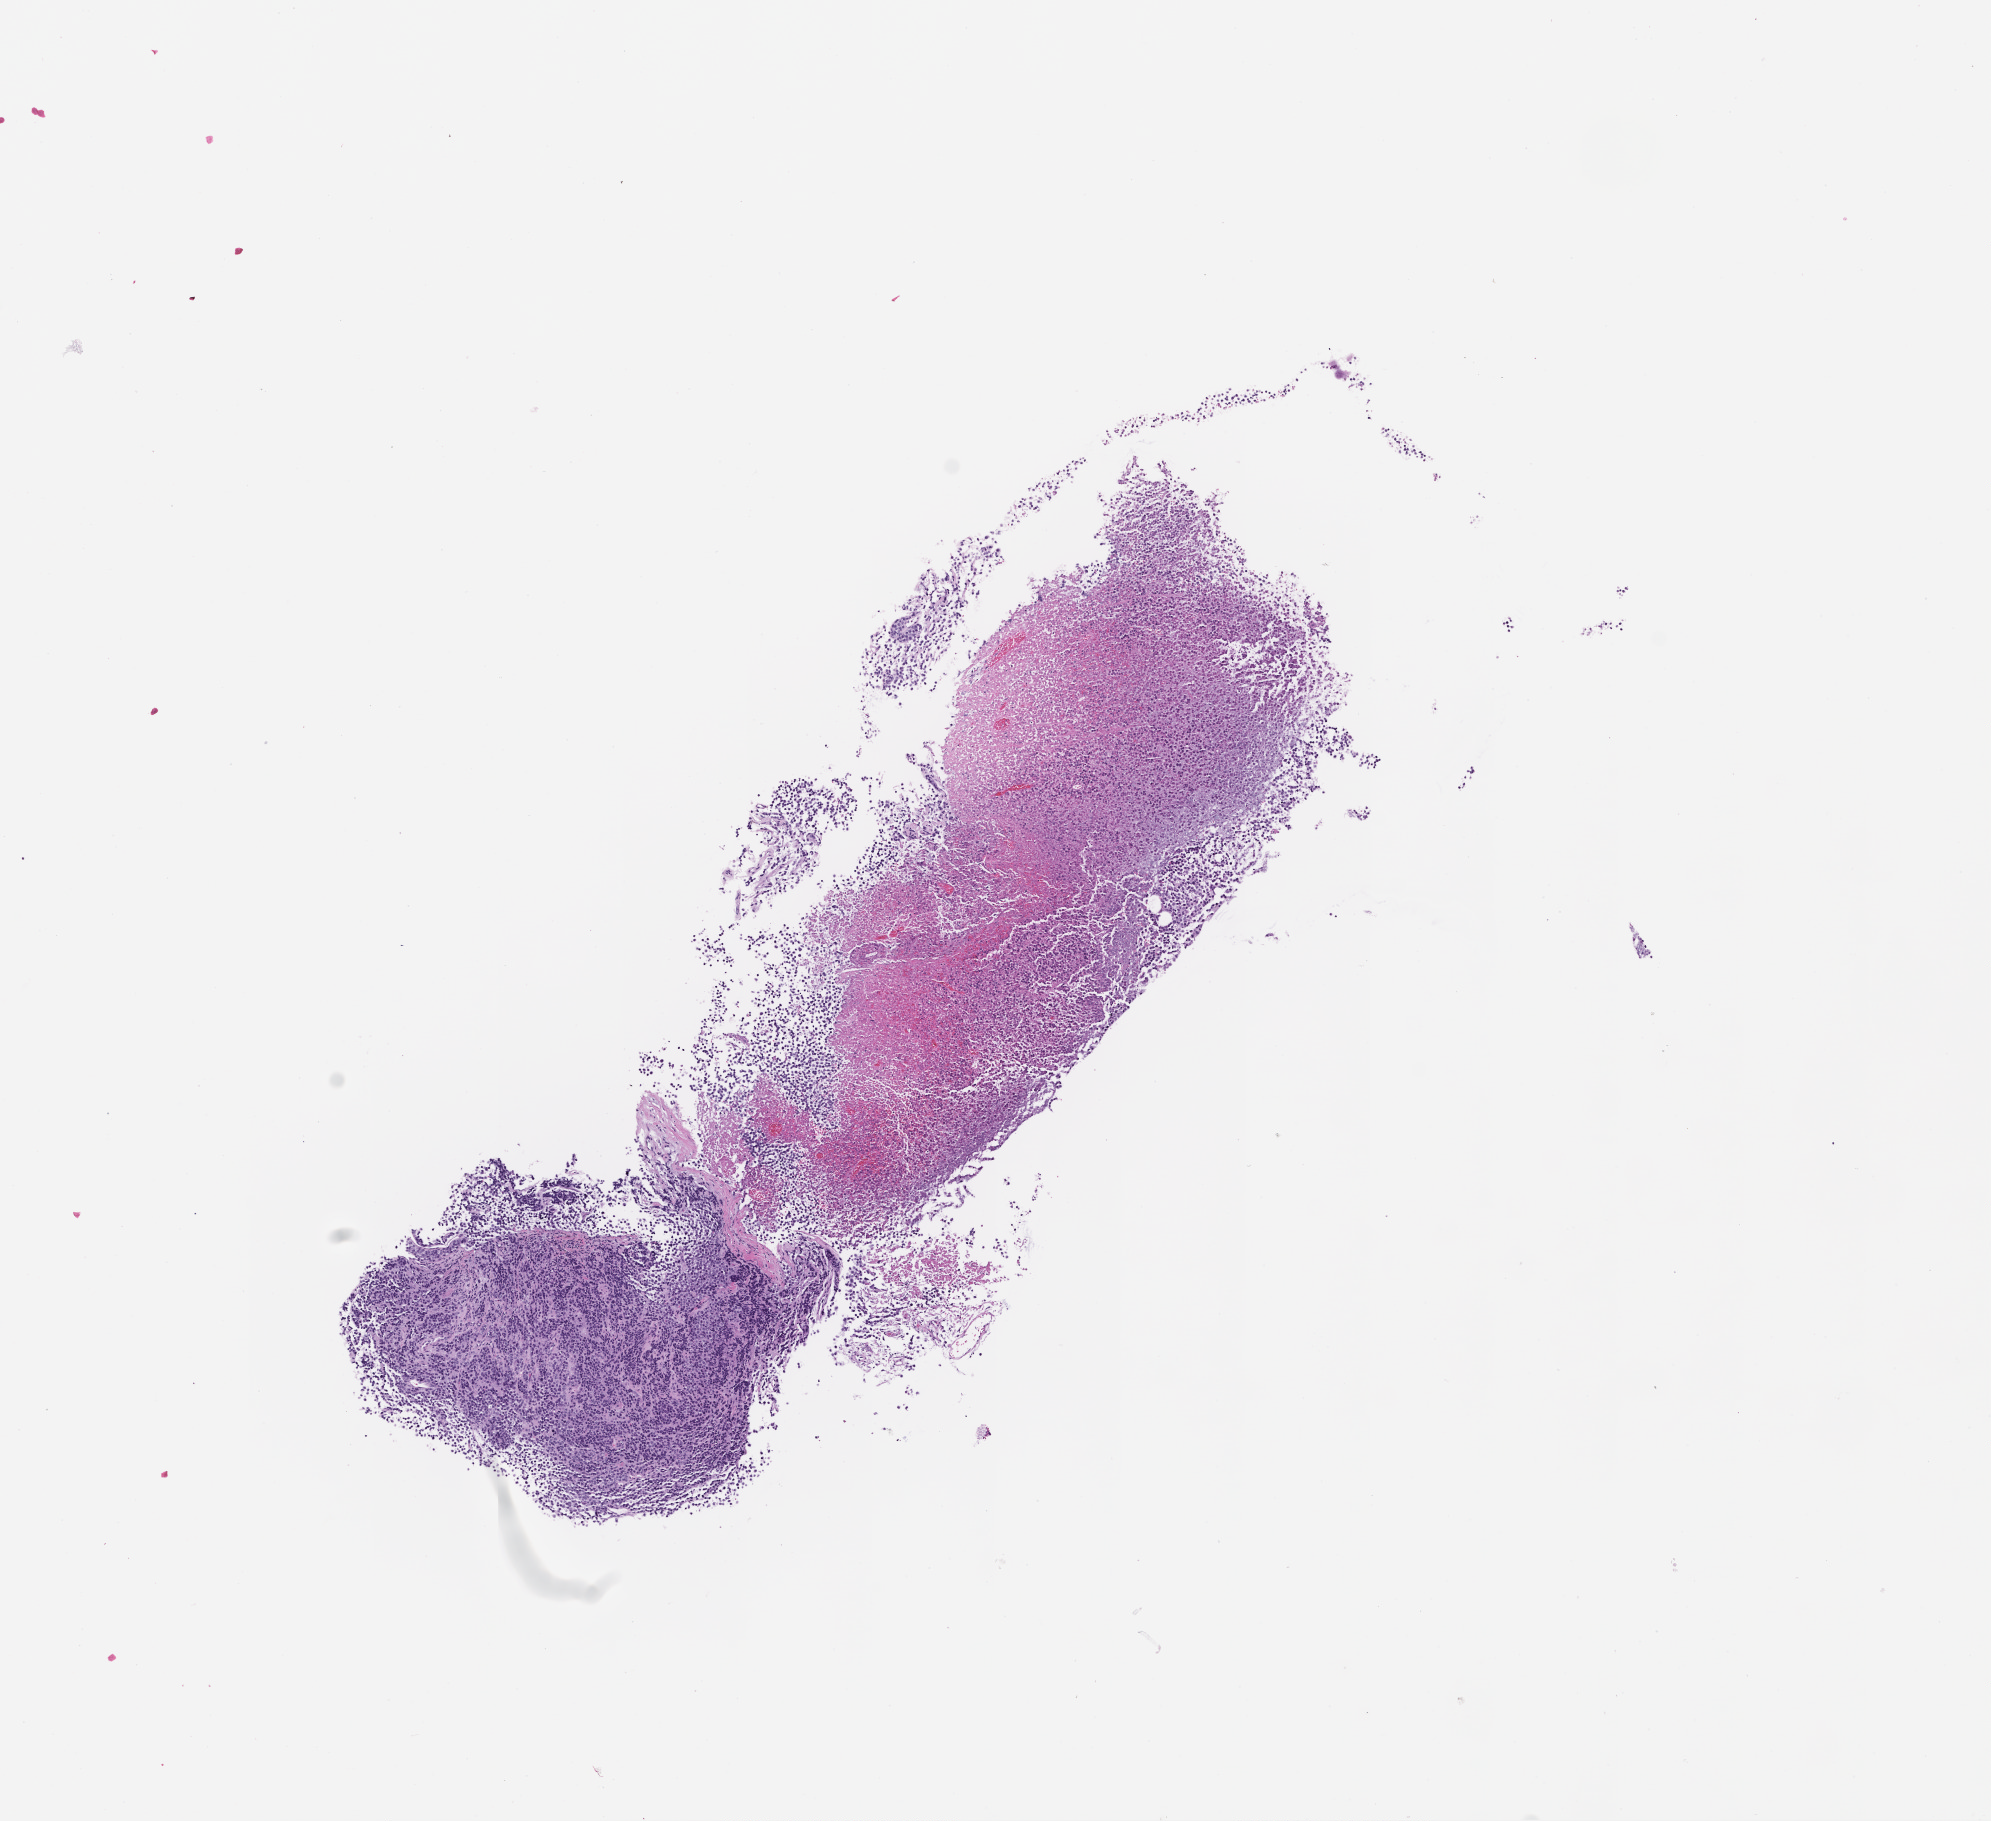
Digitized hematoxylin and eosin (H&E)-stained section, a low-resolution overview of the entire scanned area, about 8.0 x 7.4 mm; formalin-fixed, paraffin-embedded (FFPE) tissue. Patient: male.
This section: metastasis (sampled organ not recorded). Patient diagnosis (primary): Melanoma.